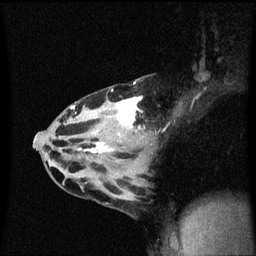
Breast MRI (dynamic contrast-enhanced), one sagittal slice; slice 32 of 60 in the series (ordered by position); dynamic contrast-enhanced series, image 2 of 3 at this slice position (ordered by acquisition); 1.5 T; TE 4.2 ms, TR 8.4 ms; 2 mm slice thickness; 256 × 256 image matrix. Patient: female, 32 years.
Structures marked on this image (semi-automatically segmented with operator editing):
- analysis volume of interest (the breast-tissue region the enhancement analysis was run in; not a lesion): bounding box (x1, y1, x2, y2) in pixels: (55, 78, 157, 167)
- tumour enhancement mask (voxels above the 70 % enhancement threshold inside the analysis volume of interest): (71, 82, 145, 155)